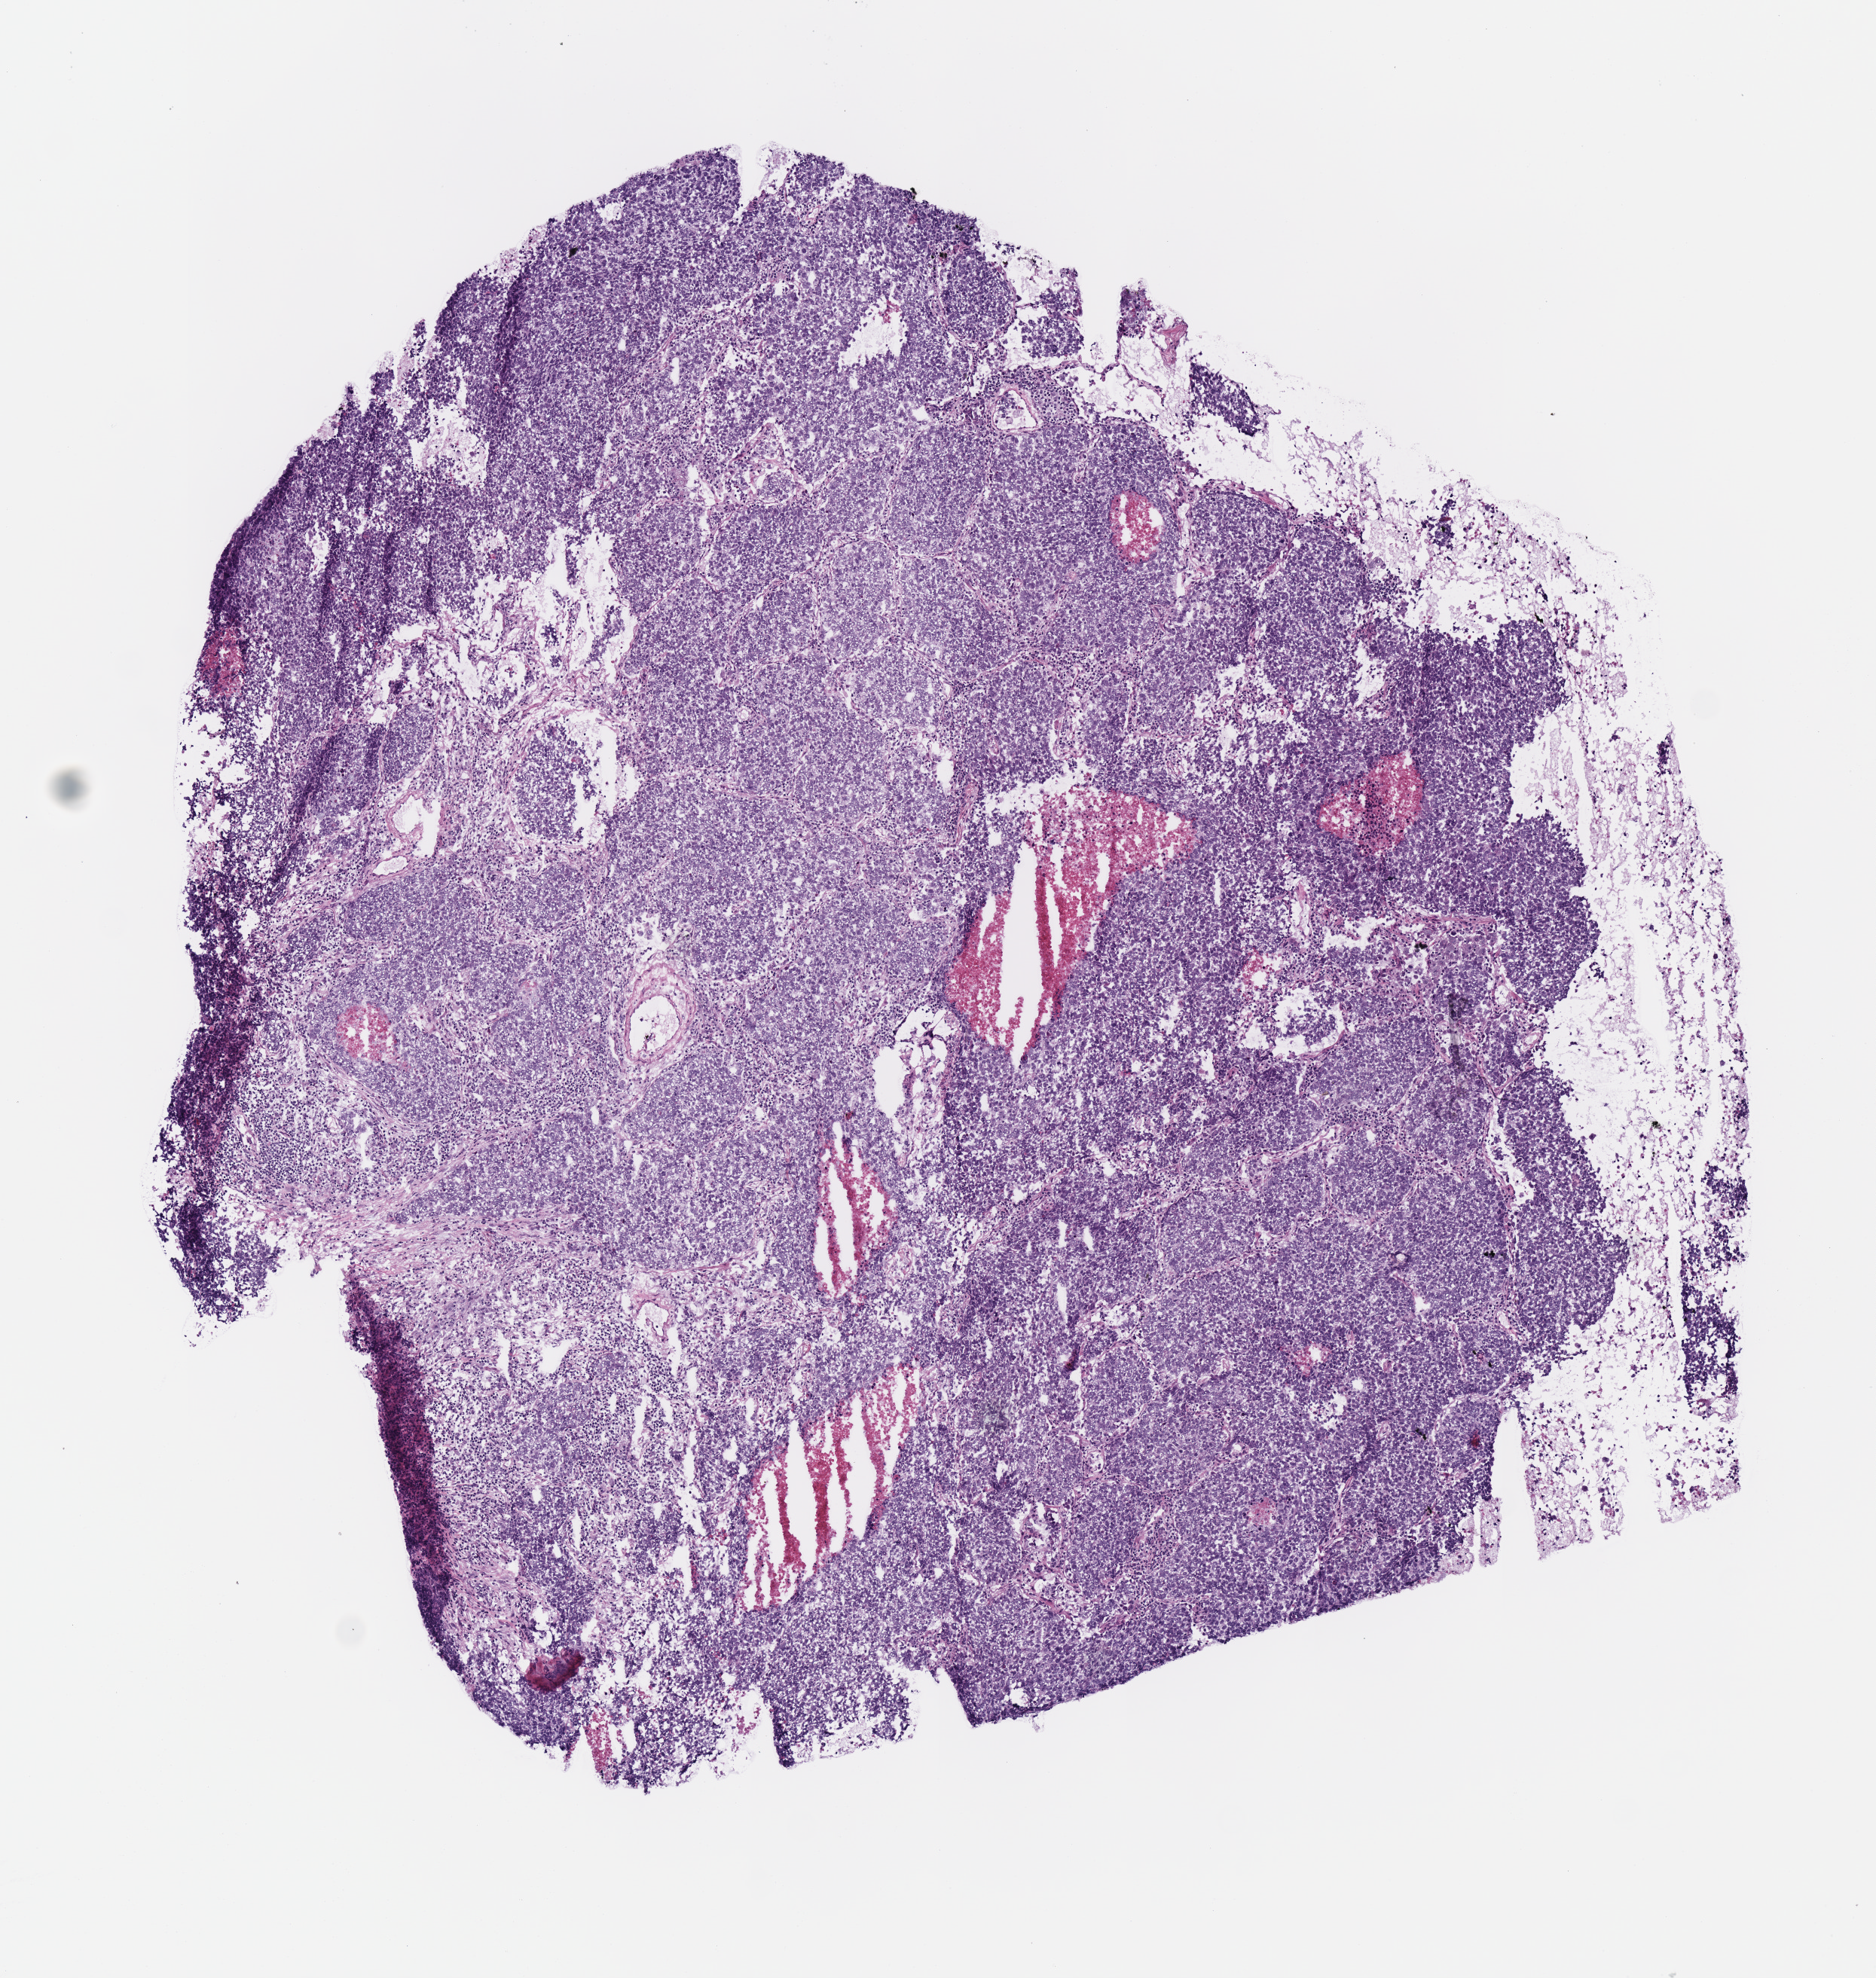
Whole-slide histology image, H&E-stained, a low-resolution overview of the entire scanned area, about 4.9 x 5.2 mm (from a 40x scan). Frozen section. Sample: primary tumour, lung. Female, age 75 years at initial diagnosis. Pathologist review of this section (percent, as recorded): tumour cells 87%, tumour nuclei 75%, normal cells 0%, stromal cells 5%, necrosis 8%.
AJCC pathologic stage: IA. Diagnosis: Squamous cell carcinoma, NOS (upper lobe, lung).